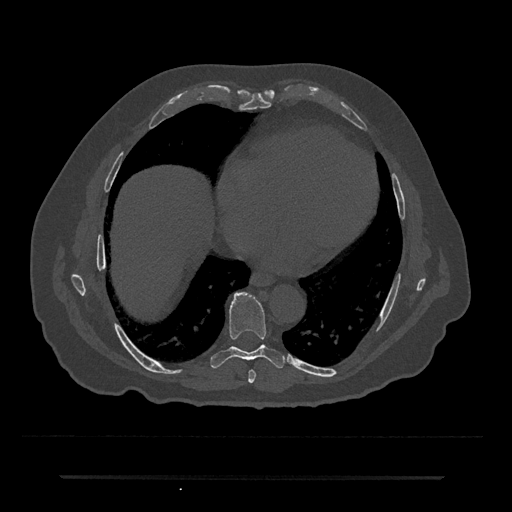
CT including the spine, one axial slice; slice 335 of 797 in the series (ordered by position); reconstruction kernel Br40s/3; 120 kVp; bone window (W 1800 / L 400 HU); 0.5 mm slice thickness; 512 × 512 image matrix, field of view 437 × 437 mm. Male patient, age 69 years. Case-level facts recorded for this patient, not image findings: primary cancer: prostate.
Structures marked on this image (semi-automatic segmentation, software-assisted and operator-edited):
- T7 vertebra: box from (x=248, y=370) to (x=256, y=383) px
- T8 vertebra: (x=211, y=293)–(x=285, y=369)